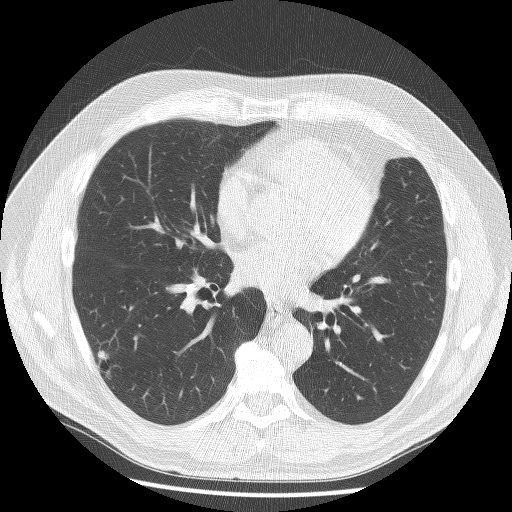
Axial slice from a low-dose chest CT screening exam; first (baseline) screen; lung window (W 1500 / L -600 HU); 2.5 mm slice thickness; slice 93 of 179 in the series; 512 × 512 image matrix, field of view 375 × 375 mm. Male participant, aged 61 years at enrolment. Former smoker at enrolment.
Expert-annotated lung lesion, bounding box [x1, y1, x2, y2] px = [80, 340, 133, 392]. The exam's reader record, not a measurement of the box and not confirmed to be the same lesion: non-calcified nodule or mass ≥4 mm, right lower lobe, 10 × 8 mm, spiculated (stellate) margins, soft tissue attenuation. Official screen result: positive, change unspecified: nodule(s) >= 4 mm or enlarging nodule(s), mass(es), or other non-specific abnormalities suspicious for lung cancer.